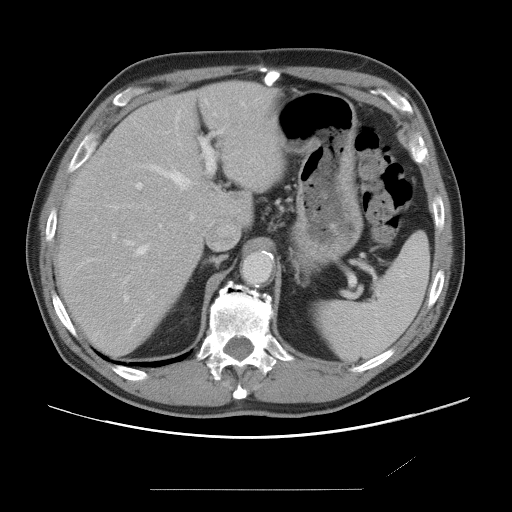
Contrast-enhanced abdominal CT, one axial slice. Position 50 of 87 along the scan axis. 120 kVp. Soft-tissue window (W 400 / L 40 HU). 512 × 512 image matrix, field of view 406 × 406 mm. Male patient, age 74 years. Case-level facts recorded for this patient, not image findings: diagnosis: colorectal cancer liver metastases, imaged before liver resection; multiple liver metastases: yes; largest metastasis: 1.1 cm; disease in both lobes: no.
Annotated regions visible in this slice (expert manual segmentation):
- hepatic veins: bounding box (x1, y1, x2, y2) in pixels: (126, 113, 216, 328)
- liver: (55, 82, 282, 357)
- planned liver remnant (the part of the liver to remain after resection): (55, 82, 282, 356)
- portal vein (with intrahepatic branches): (113, 131, 222, 302)
- liver metastasis: (228, 195, 245, 202)